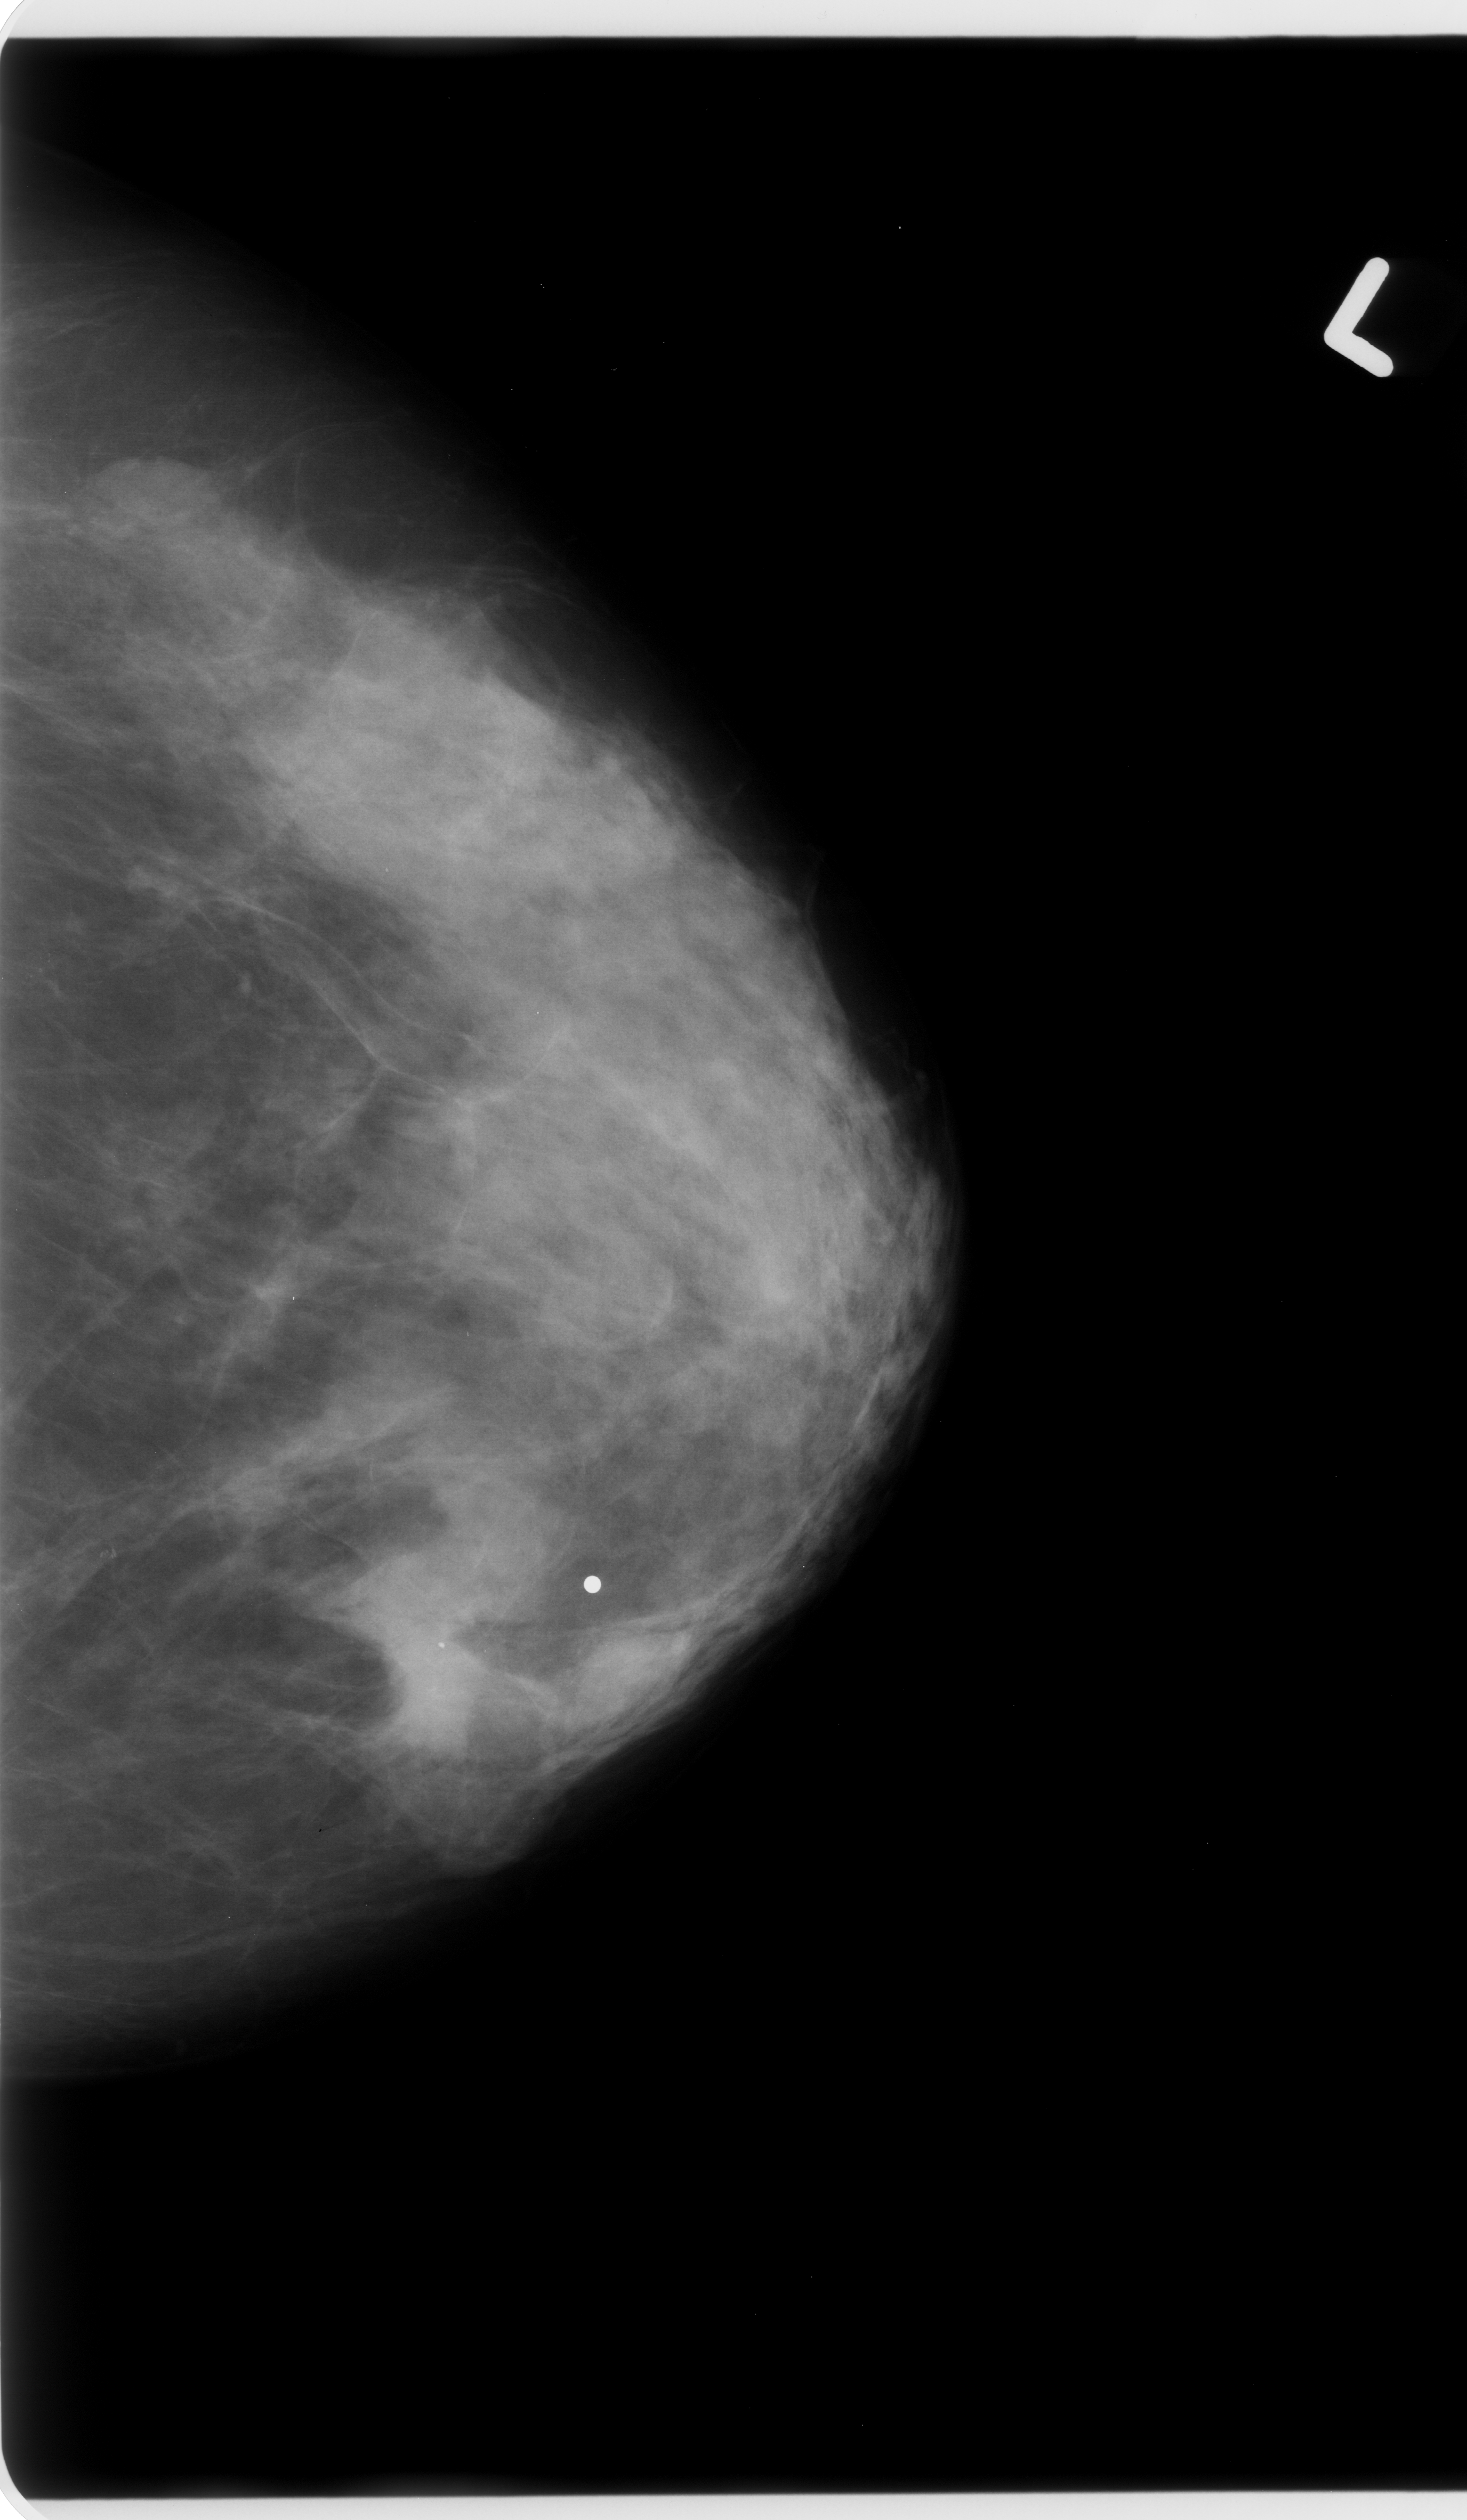
Scanned film-screen mammogram. Left breast. CC view. 1467 × 2520 image matrix.
Marked abnormalities (boxes around the expert regions of interest):
- mass, shape irregular, margins ill defined; BI-RADS assessment category 5; subtlety rating 4 on a 1 (subtle) to 5 (obvious) scale; pathology result (as recorded, not read from the image): malignant: box from (x=340, y=1582) to (x=496, y=1749) px